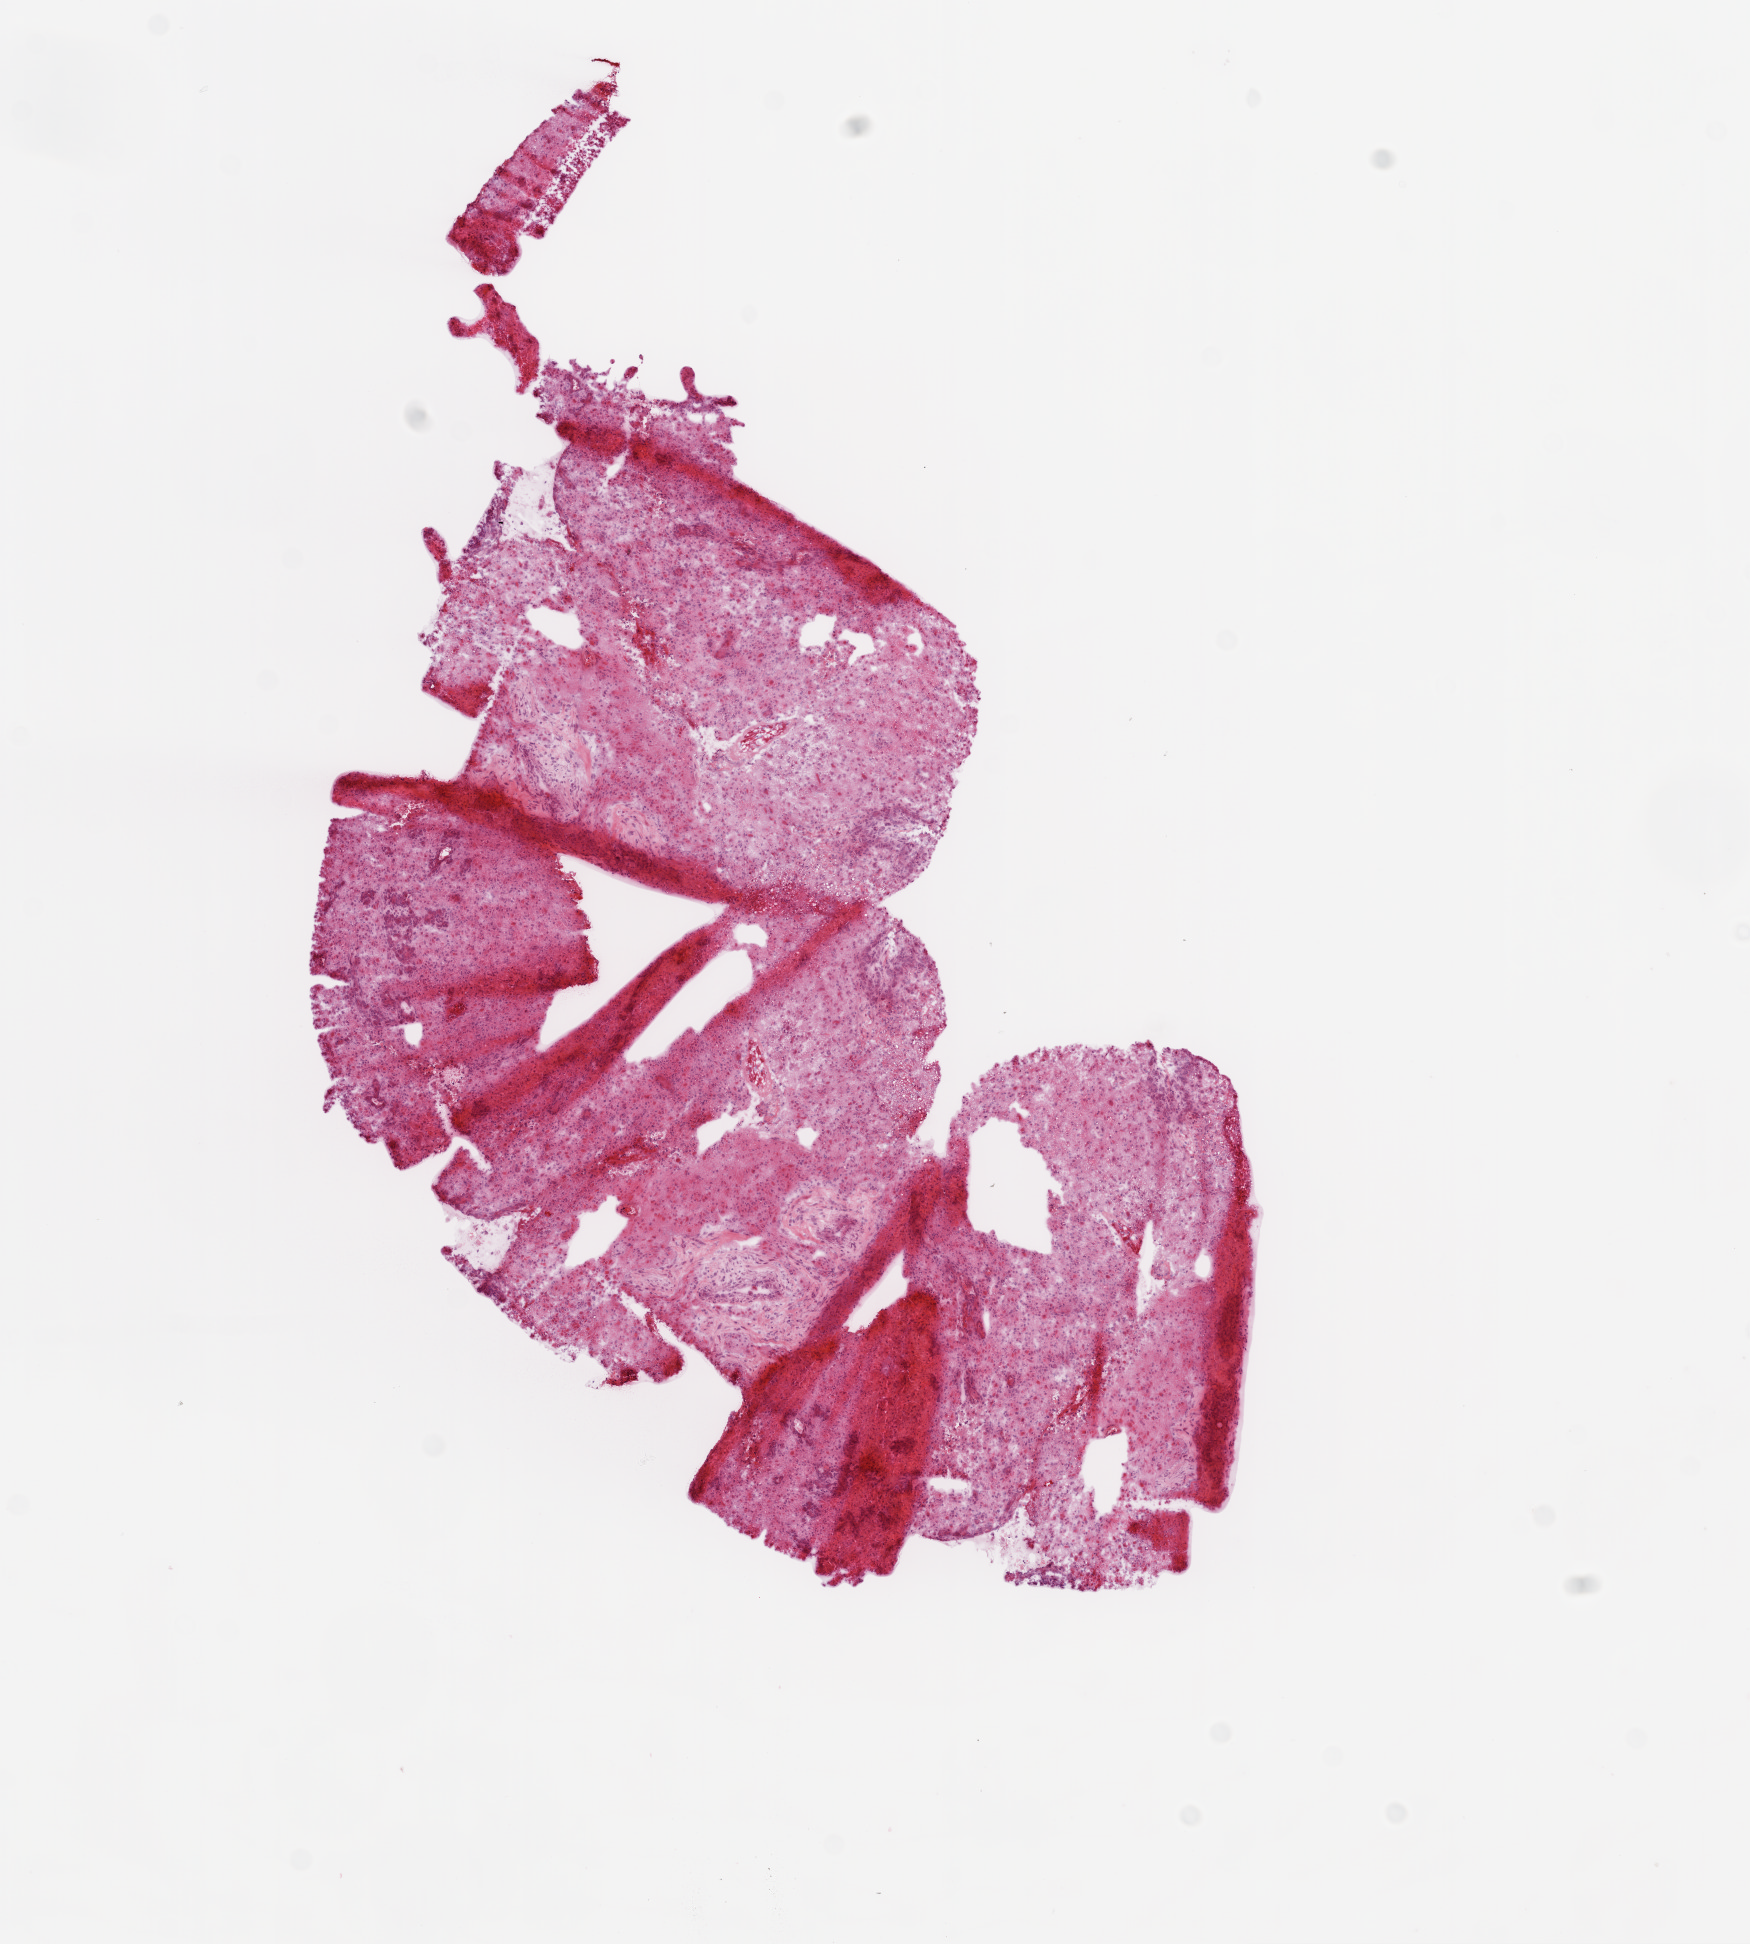
Whole-slide histology image, H&E-stained — low-resolution overview of the scanned area, about 7.0 x 7.8 mm (acquisition: 20x scan), frozen section, sample: primary tumour, brain. Patient: male, age at initial diagnosis 48 years. Composition of this section per pathologist review: tumour cells 85%, tumour nuclei 80%, normal cells 0%, stromal cells 15%, necrosis 0%.
Pathologic diagnosis: Glioblastoma.